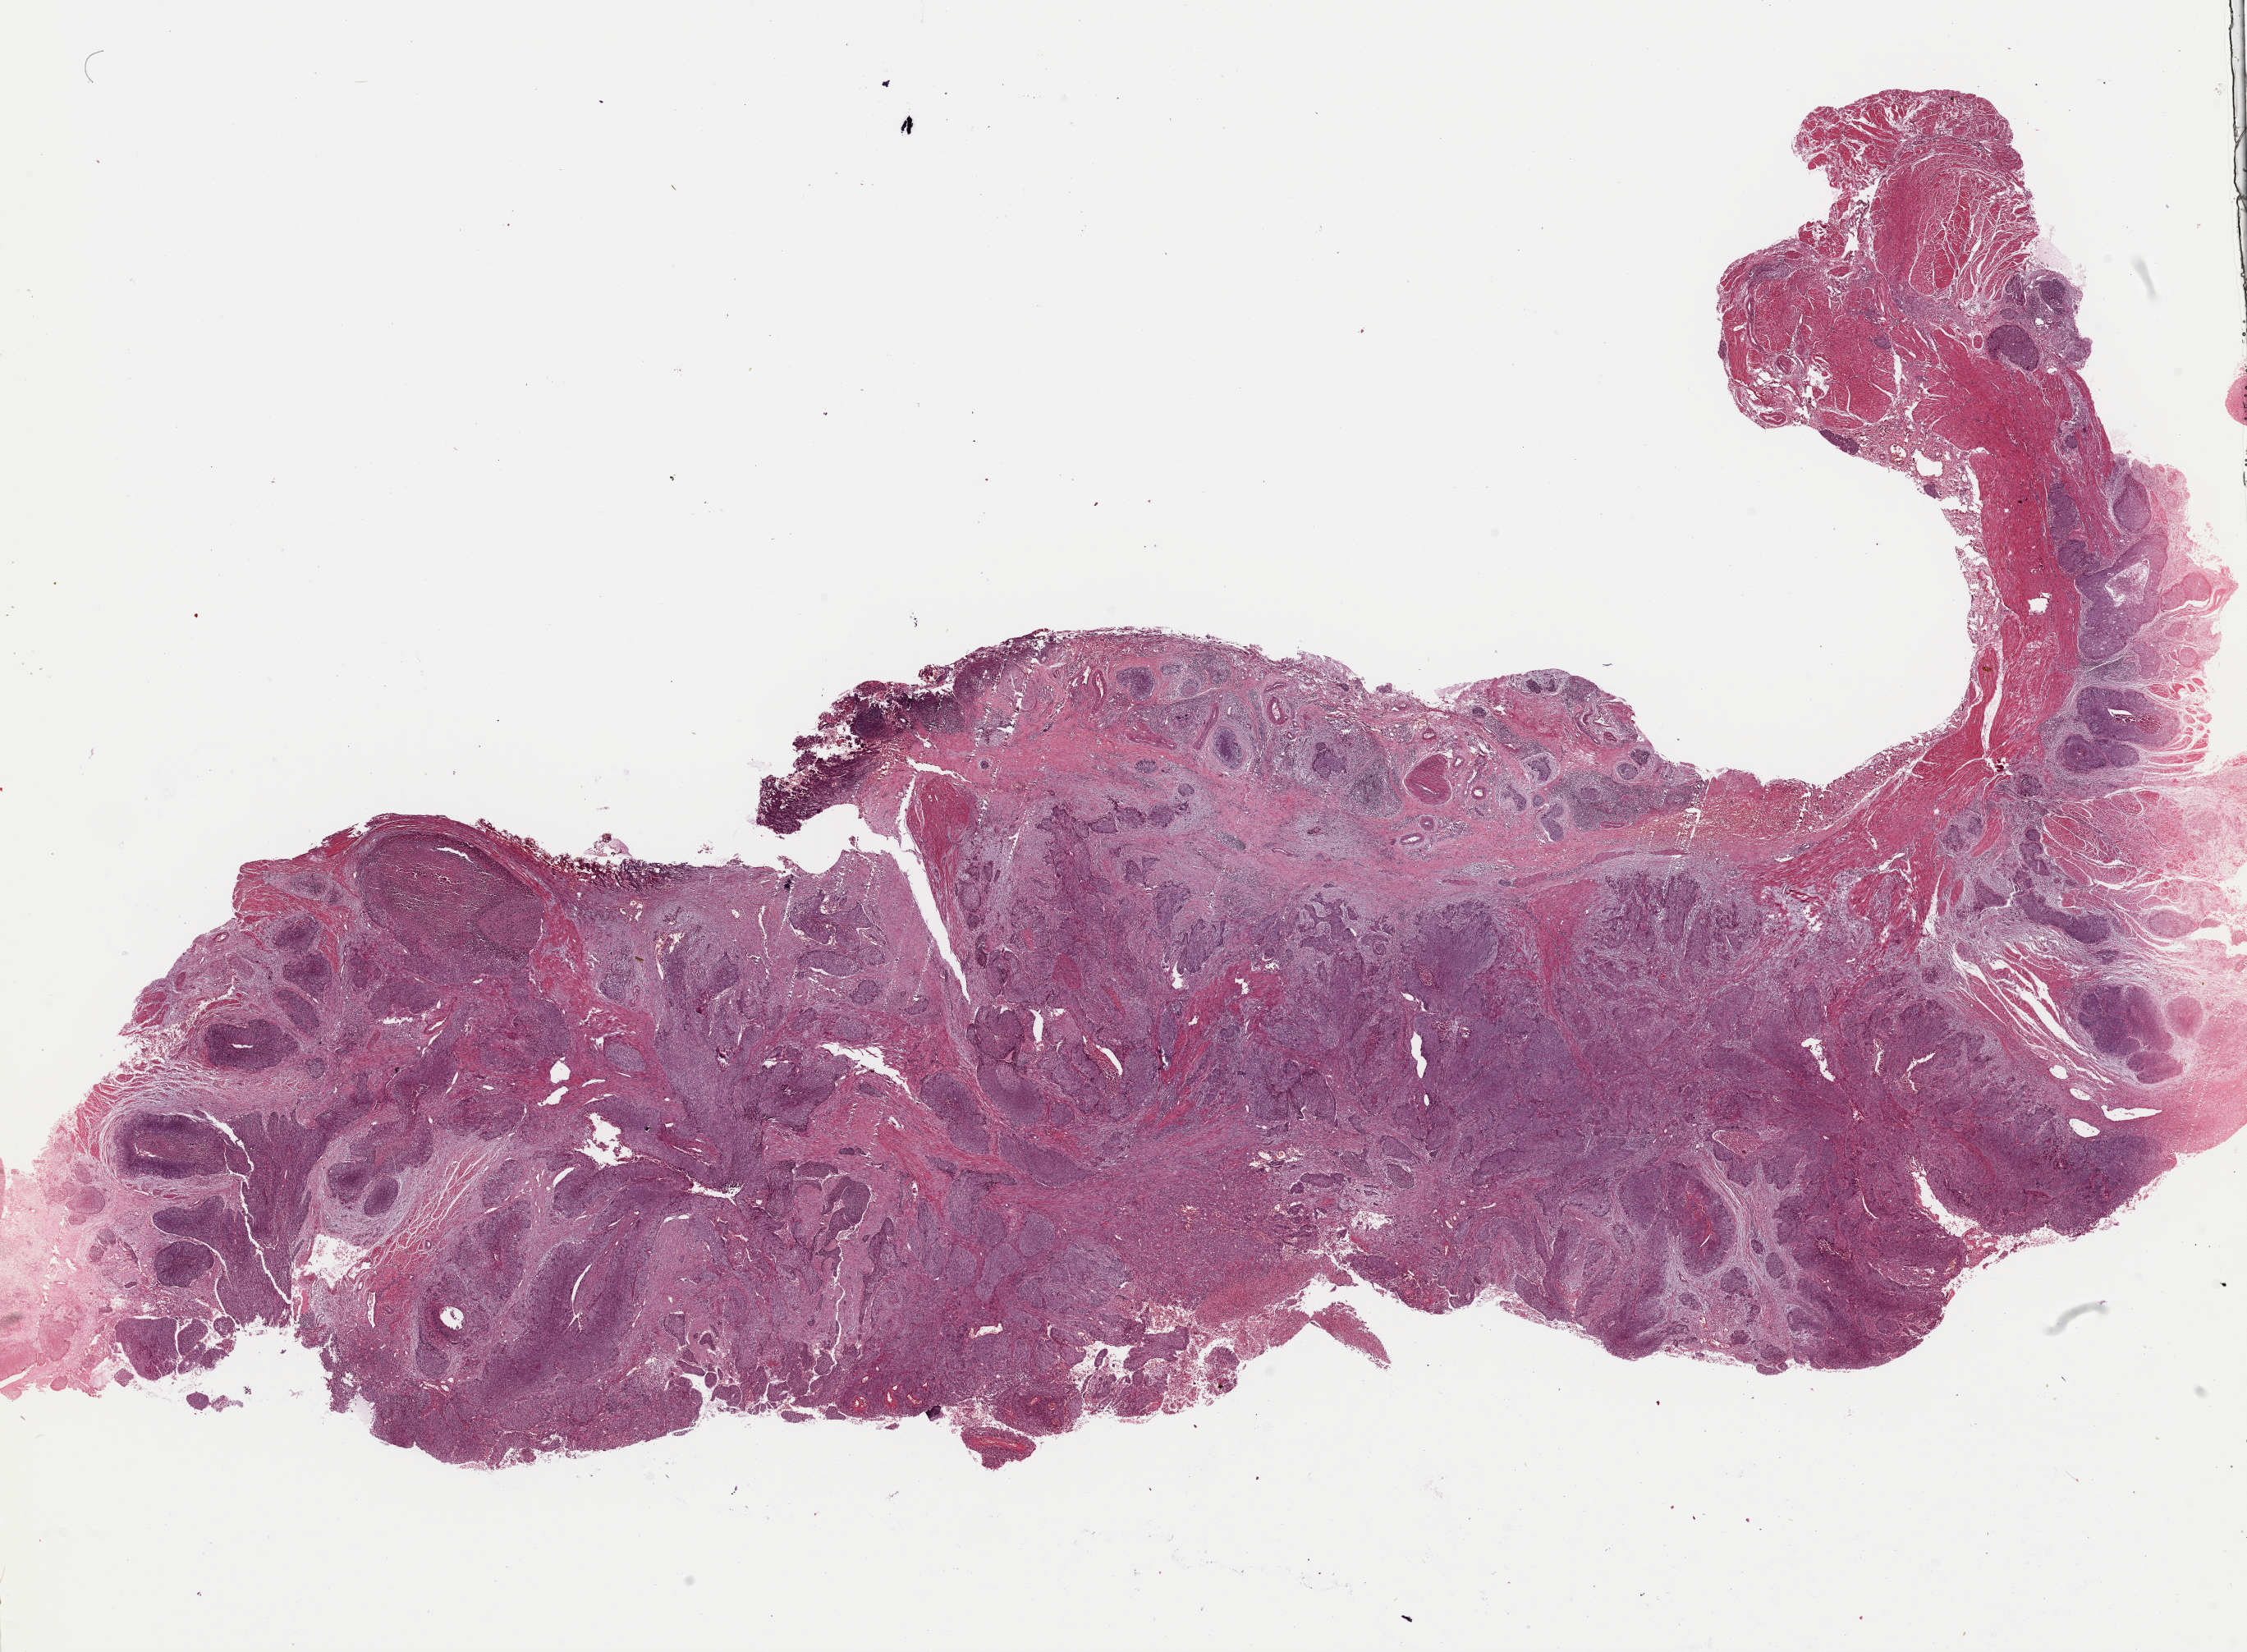
Digitized H&E-stained tissue section (whole slide), shown as a low-resolution overview of the whole scanned area (about 21.6 x 15.9 mm, acquisition: 40x scan), FFPE section, primary tumour sample from the esophagus. Male patient; age at initial diagnosis 46 years. Histologic grade: G3 (poorly differentiated).
* AJCC pathologic stage: III (6th edition)
* lymph nodes positive (case pathology): 2 of 2 examined
* histologic diagnosis: Squamous cell carcinoma, NOS